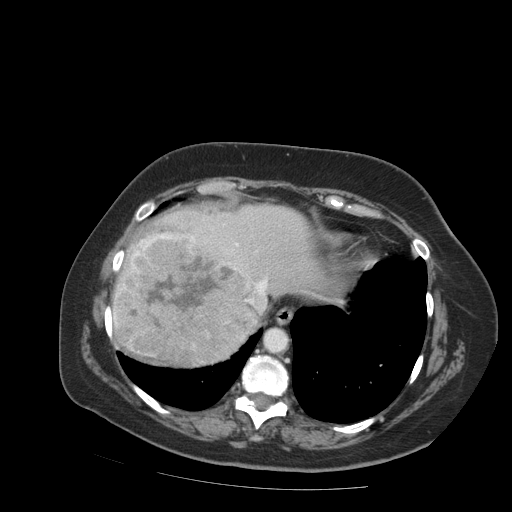
Contrast-enhanced abdominal CT (liver protocol), one axial slice; position 74 of 99 along the scan axis; 140 kVp; soft-tissue window (W 400 / L 40 HU); 2.5 mm slice thickness; 512 × 512 image matrix. From the clinical record (not read from this slice): diagnosis: hepatocellular carcinoma (patient treated with transarterial chemoembolisation; whether this scan precedes or follows treatment is not stated here); TNM stage (as recorded): Stage-IVB; Child-Pugh class: A; tumour nodularity: uninodular.
Outlined on this slice (semi-automatically segmented with operator editing):
- liver parenchyma outside the tumour (the mass and vessels are separate outlines, so this box may not span the whole liver): bounding box (x1, y1, x2, y2) in pixels: (114, 204, 332, 354)
- mass: (110, 230, 267, 368)
- liver vessels: (193, 236, 268, 304)